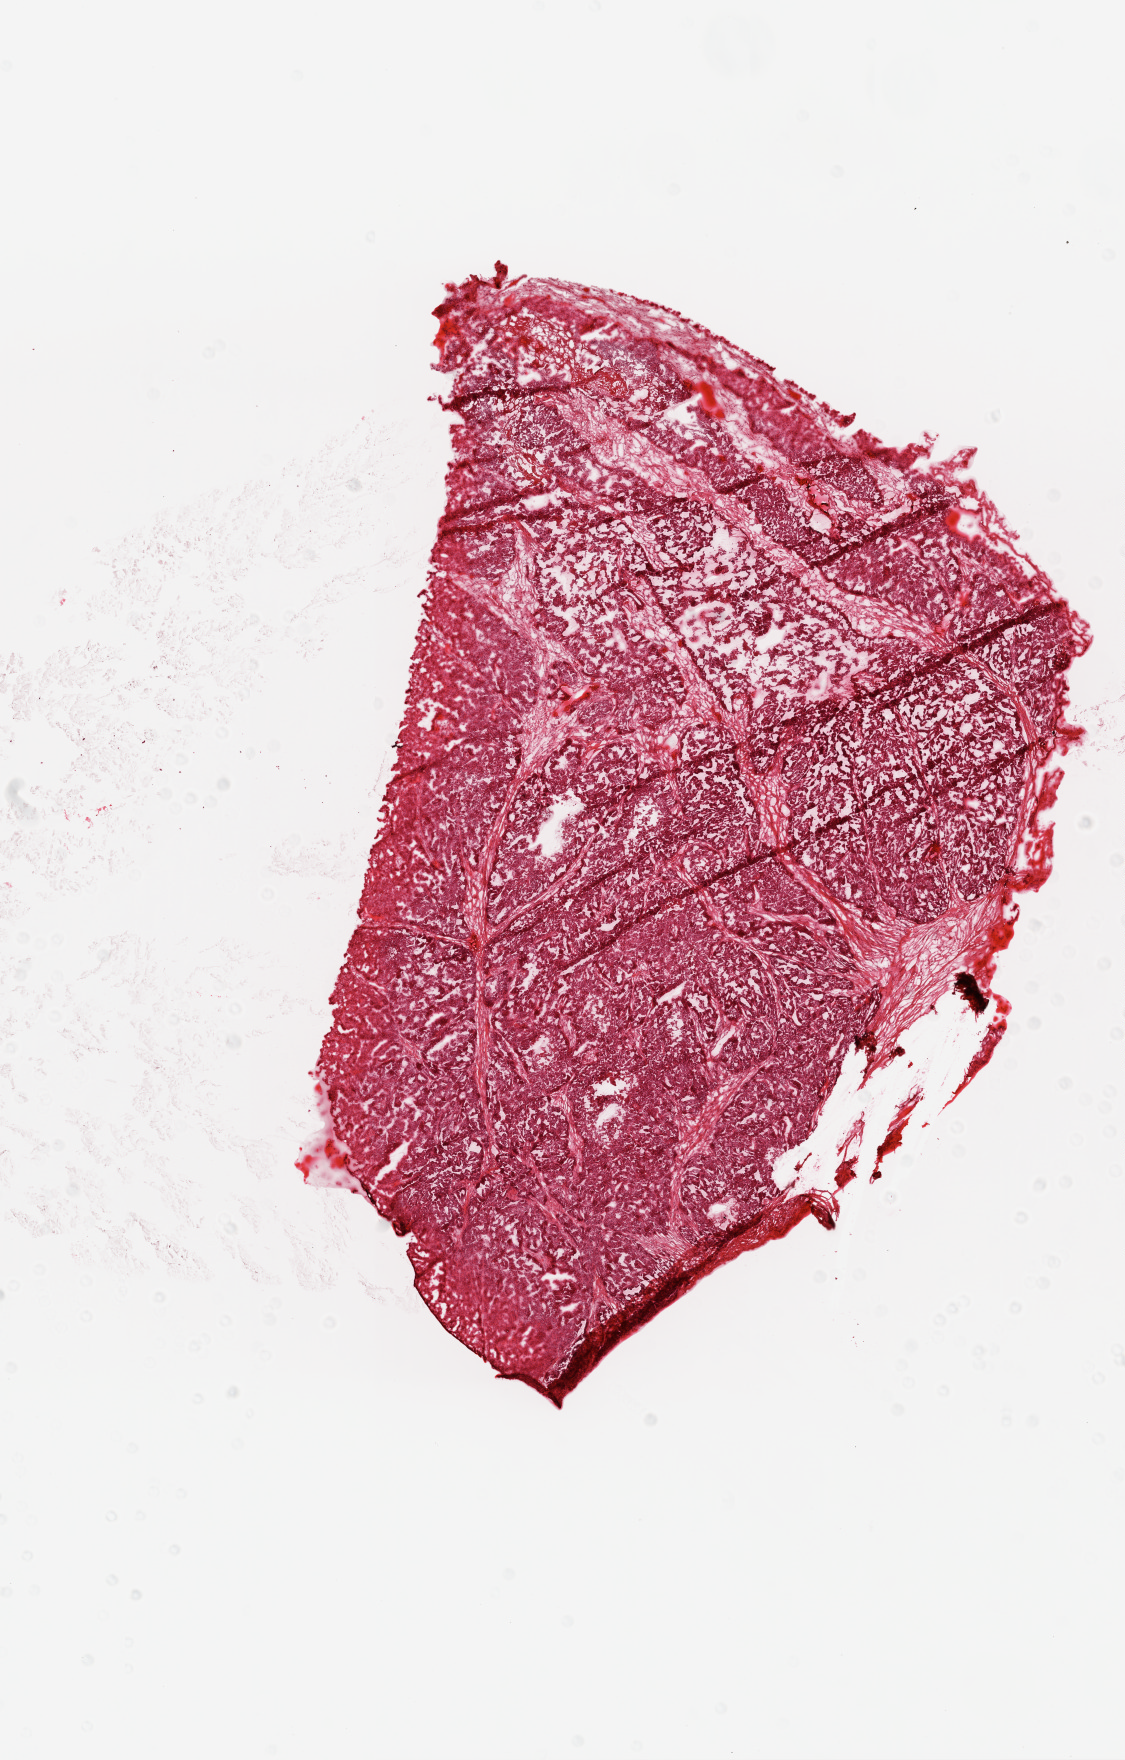
H&E-stained whole-slide image — a low-resolution overview of the entire scanned area, about 9.0 x 14.1 mm, frozen section from the top of the tissue portion, sample: primary tumour, ovary. Female, age 53 years at initial diagnosis. Histologic grade: G3 (poorly differentiated). Composition of this section per pathologist review: tumour cells 90%, tumour nuclei 99%, normal cells 0%, stromal cells 5%, necrosis 5%.
* histologic diagnosis: Serous cystadenocarcinoma, NOS
* FIGO stage: IIIC